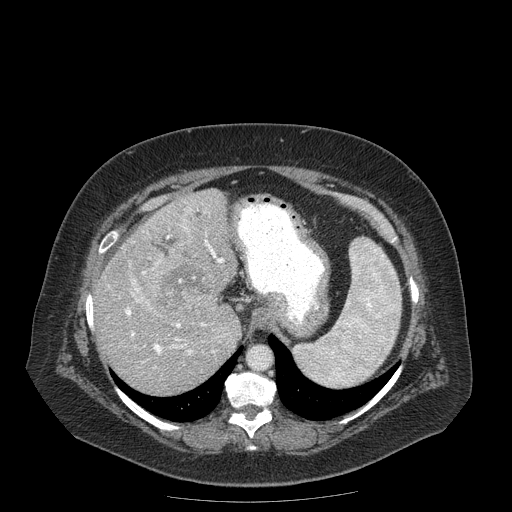
Contrast-enhanced abdominal CT (liver protocol), one axial slice; slice 133 of 204 in the series (ordered by position); 120 kVp; soft-tissue window (W 400 / L 40 HU); 2.5 mm slice thickness; 512 × 512 image matrix. Case-level facts recorded for this patient, not image findings: diagnosis: hepatocellular carcinoma (patient treated with transarterial chemoembolisation; whether this scan precedes or follows treatment is not stated here); TNM stage (as recorded): Stage-IIIB; Child-Pugh class: A; tumour nodularity: uninodular.
Outlined on this slice (semi-automatic segmentation, software-assisted and operator-edited):
- abdominal aorta: bounding box <247,346,270,368> (left, top, right, bottom; pixels)
- liver parenchyma outside the tumour (the mass and vessels are separate outlines, so this box may not span the whole liver): <94,188,240,394>
- mass: <145,251,221,317>
- liver vessels: <125,208,227,368>